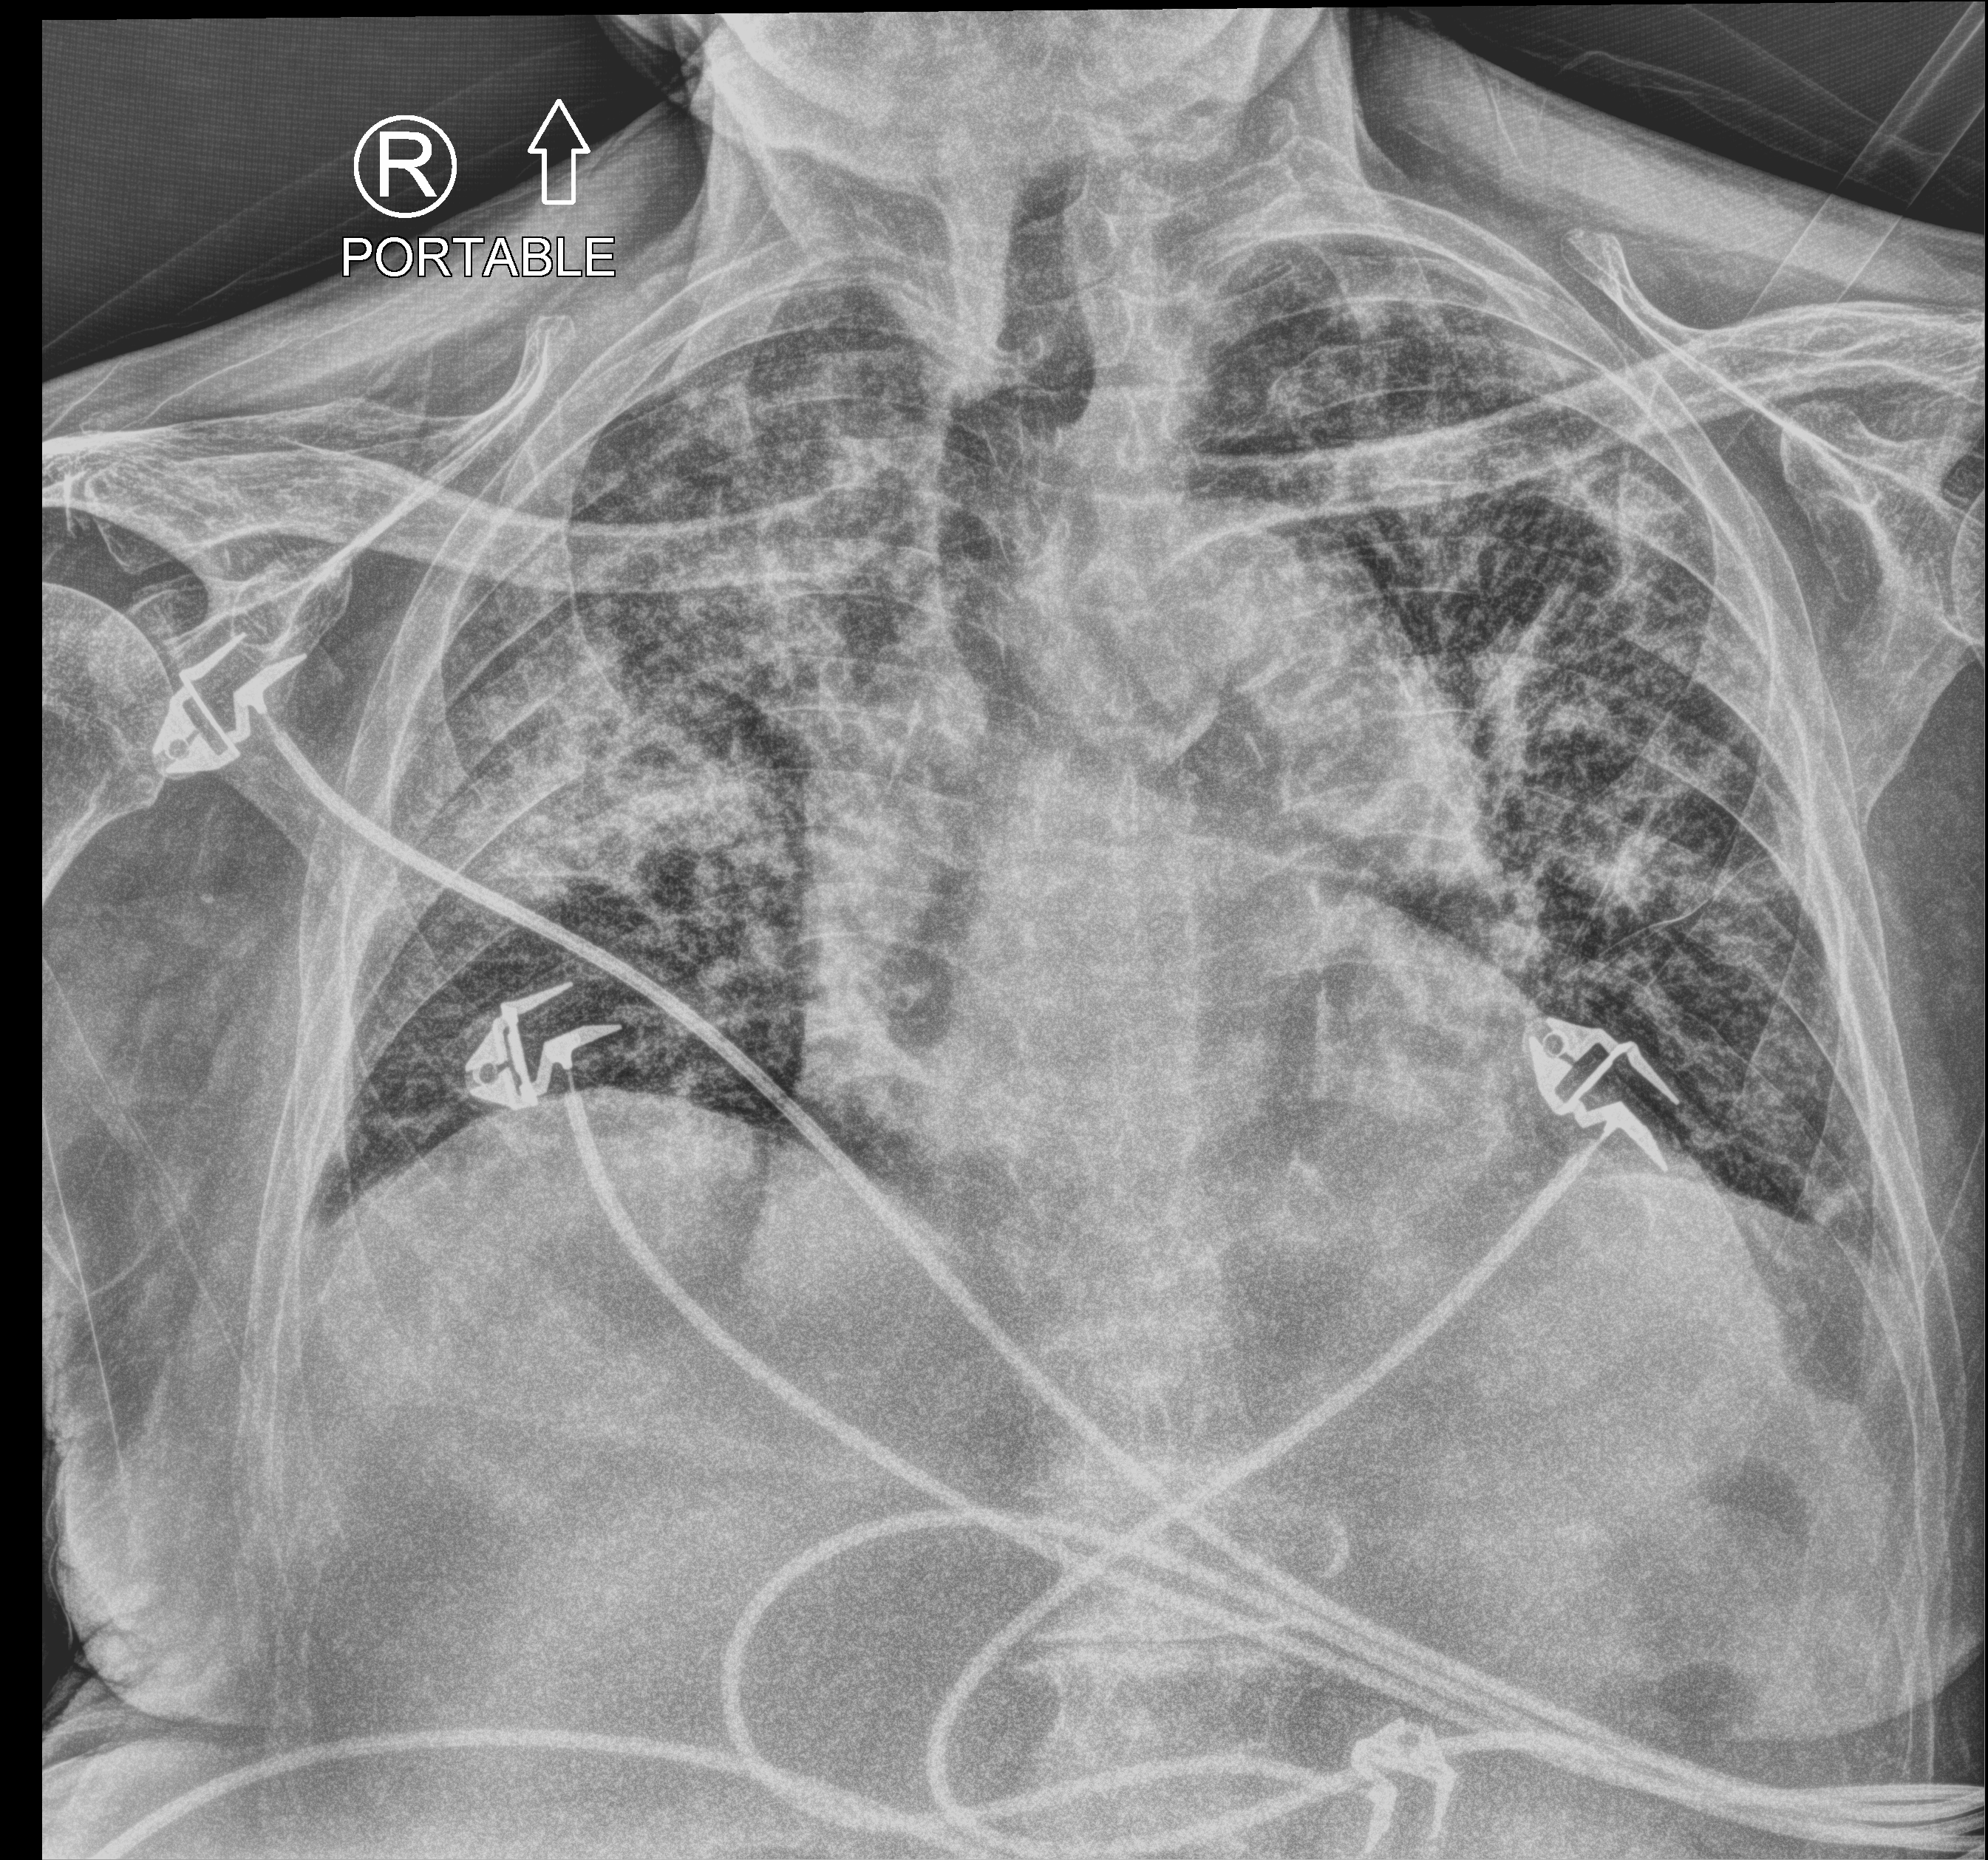
Bedside chest radiograph (computed radiography), anteroposterior (AP) projection. Male patient hospitalised with COVID-19, age 75–90 years.
From the hospital-stay record, not from the radiograph (when in the stay this image was taken is not recorded):
- length of hospital stay: 6 days
- diabetes (admission record): no
- admitted to intensive care during this hospital stay: no